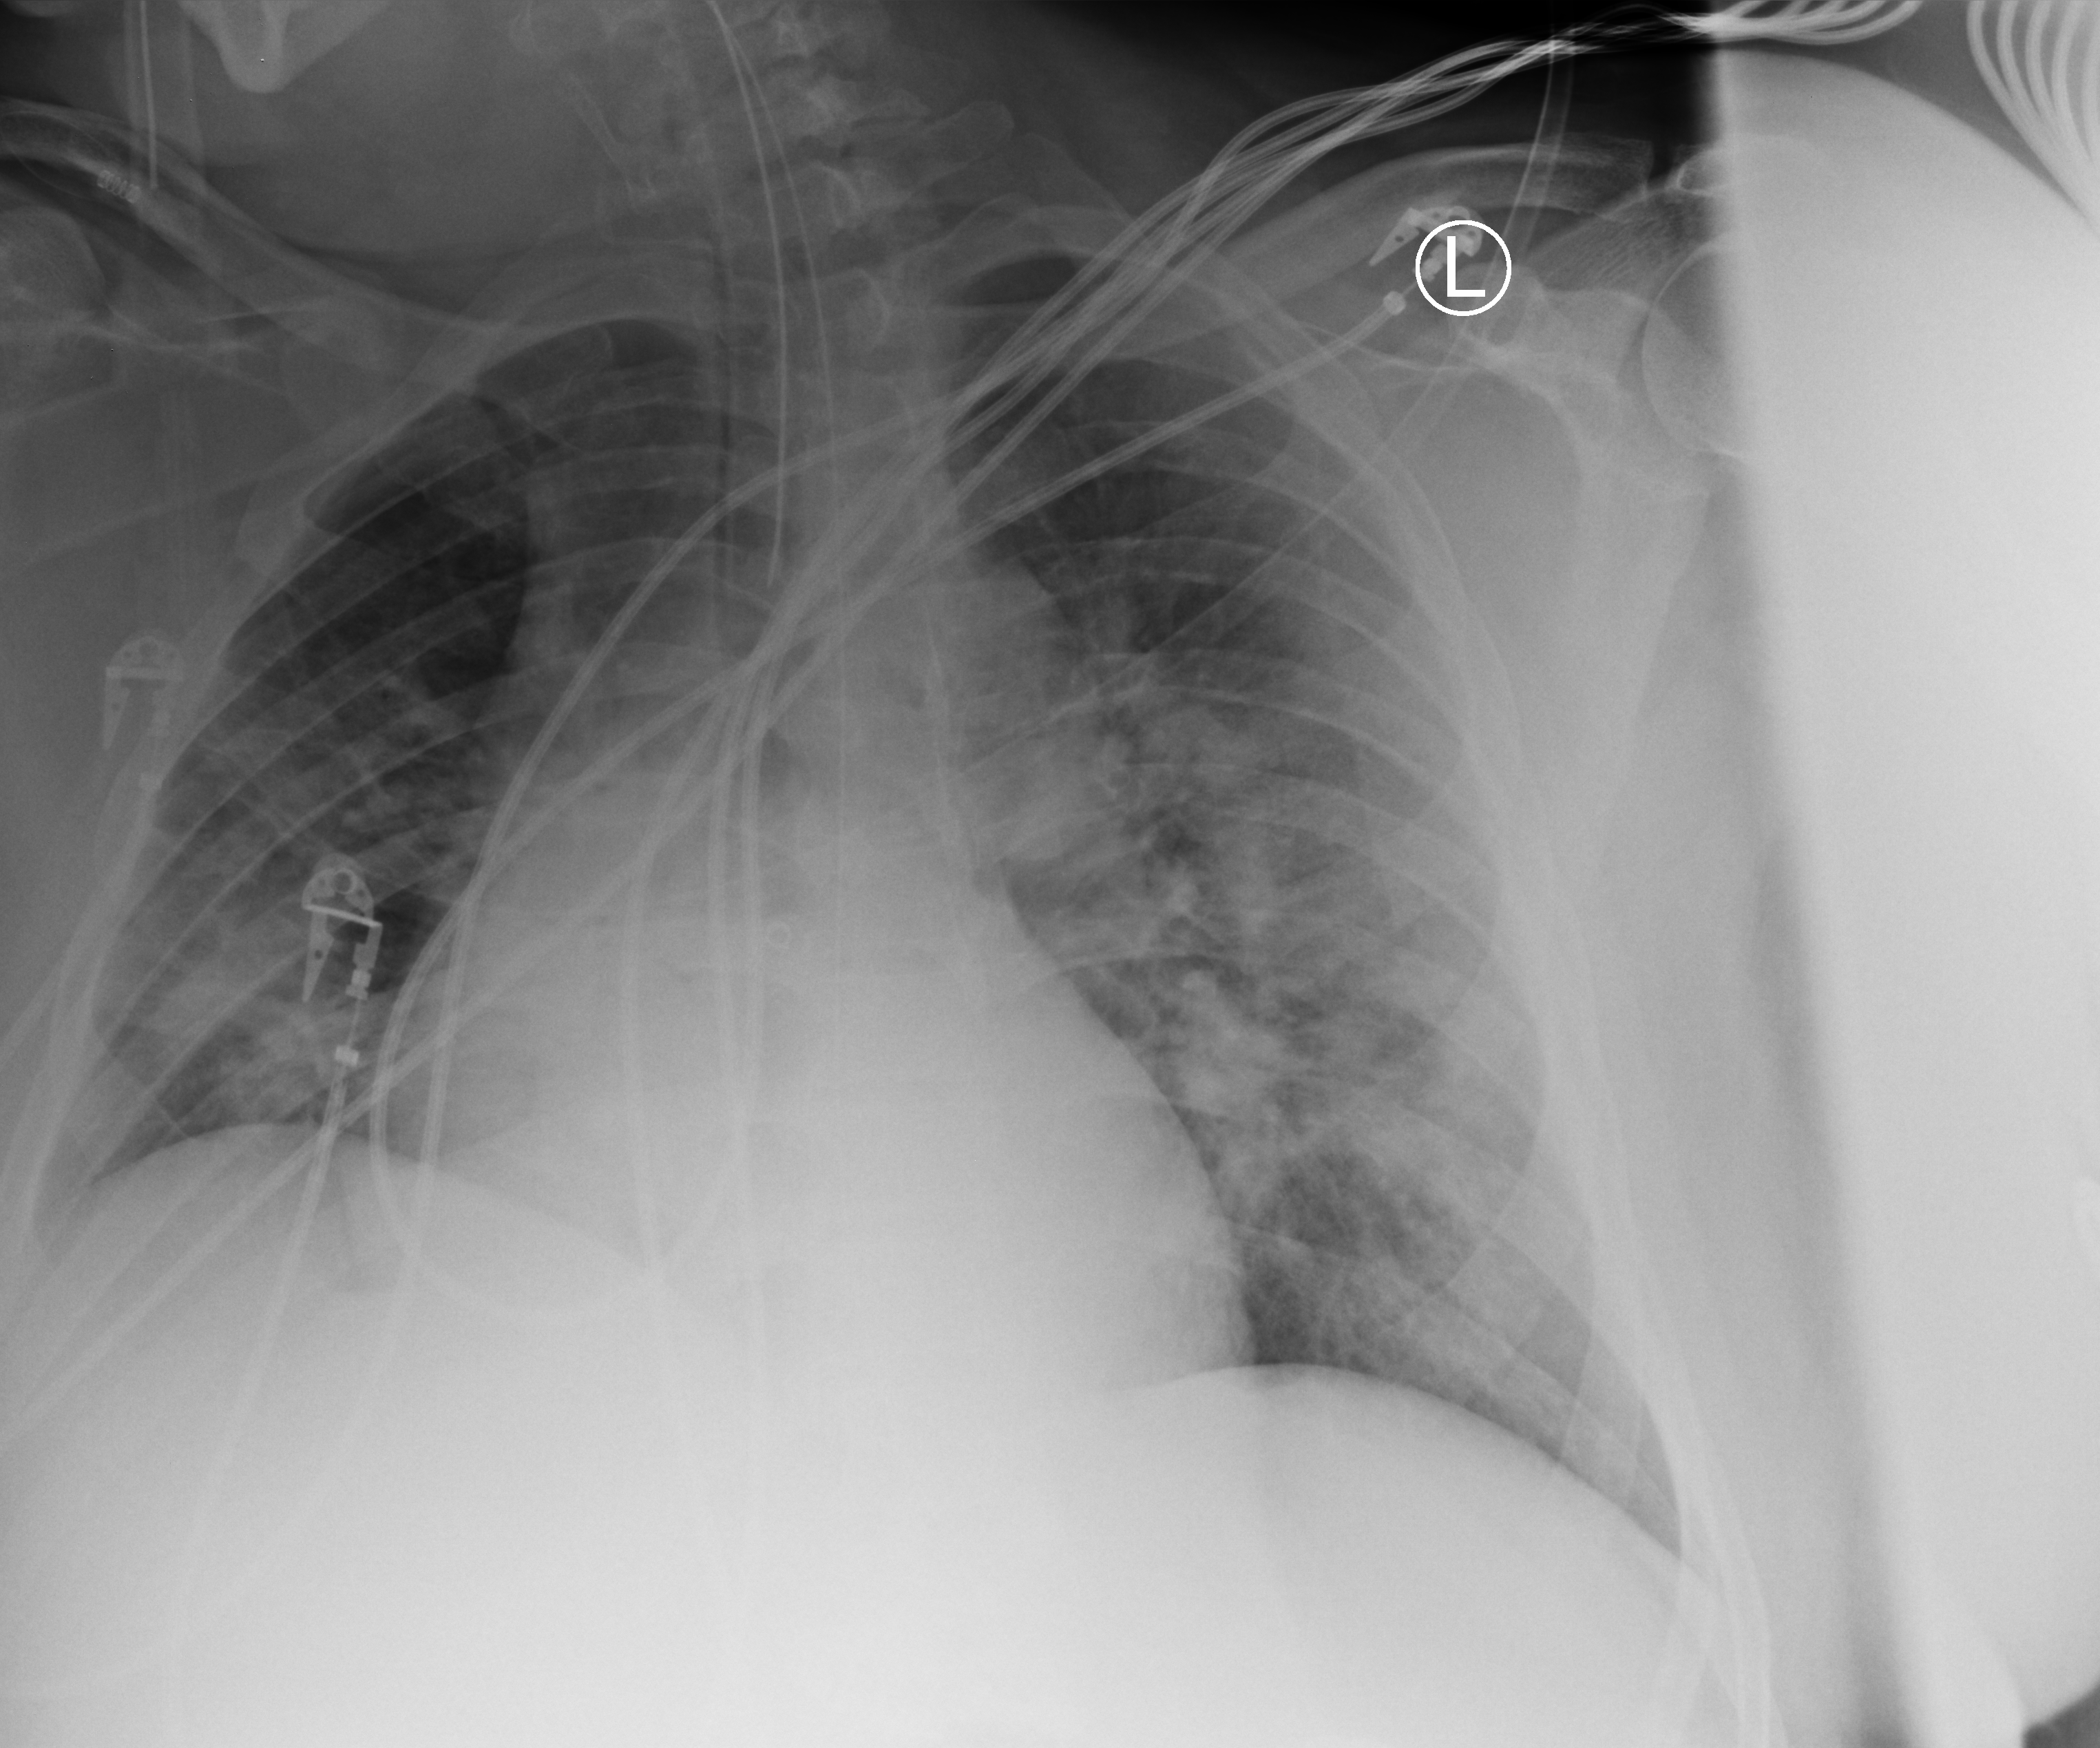
Portable chest radiograph; anteroposterior (AP) projection. Male patient hospitalised with COVID-19, age 60–74 years.
Hospital-stay facts (about this admission, not read from this image; timing relative to this image not recorded): COPD (admission record): no.